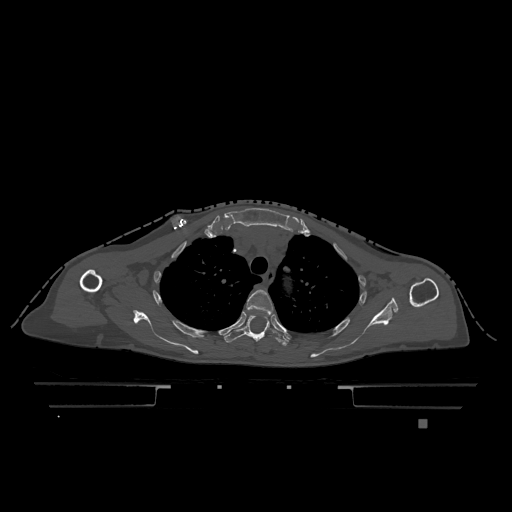
CT including the spine, one axial slice; position 898 of 1317 along the scan axis; bone window (W 1800 / L 400 HU); 0.5 mm slice thickness; 512 × 512 image matrix, field of view 500 × 500 mm. Patient: female, 74 years. From the clinical record (not read from this slice): primary cancer: lung; vertebrae with lytic lesions (as recorded): T1, T4, T5, T6, L4, L5.
Annotated regions visible in this slice (semi-automatically segmented with operator editing):
- T3 vertebra: bounding box (x1, y1, x2, y2) in pixels: (246, 289, 274, 314)
- T4 vertebra: (224, 315, 291, 346)